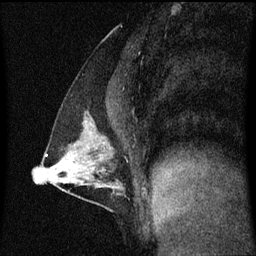
Breast MRI (dynamic contrast-enhanced), one sagittal slice. Slice 30 of 60 in the series (ordered by position). Dynamic contrast-enhanced series, image 2 of 3 at this slice position (ordered by acquisition). 1.5 T. TE 4.2 ms, TR 8.4 ms. 256 × 256 image matrix. Patient: female, 40 years. From the clinical record (not read from this slice): setting: breast cancer imaged before/during neoadjuvant chemotherapy; receptor status: triple-negative.
Outlined on this slice (semi-automatic segmentation, software-assisted and operator-edited):
- analysis volume of interest (the breast-tissue region the enhancement analysis was run in; not a lesion): bounding box (x1, y1, x2, y2) in pixels: (43, 118, 126, 195)
- tumour enhancement mask (voxels above the 70 % enhancement threshold inside the analysis volume of interest): (45, 154, 47, 157)